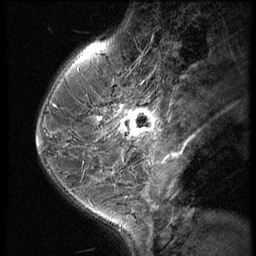
Breast MRI (dynamic contrast-enhanced), one sagittal slice; slice 21 of 60 in the series (ordered by position); 3 images stored at this slice position (order not interpretable as contrast timing); 1.5 T; TE 4.2 ms, TR 9 ms; 256 × 256 image matrix, field of view 180 × 180 mm. Patient: female, 38 years. From the clinical record (not read from this slice): setting: breast cancer imaged before/during neoadjuvant chemotherapy; receptor status: triple-negative.
Structures marked on this image (semi-automatically segmented with operator editing):
- analysis volume of interest (the breast-tissue region the enhancement analysis was run in; not a lesion): box from (x=119, y=93) to (x=165, y=150) px
- tumour enhancement mask (voxels above the 140 % enhancement threshold inside the analysis volume of interest): (x=119, y=108)–(x=161, y=140)